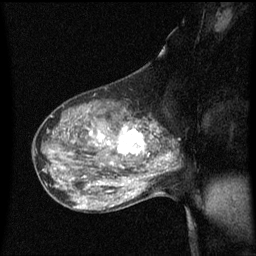
Breast MRI (dynamic contrast-enhanced), one sagittal slice. Position 37 of 60 along the scan axis. Dynamic contrast-enhanced series, image 2 of 3 at this slice position (ordered by acquisition). 1.5 T. TE 4.2 ms, TR 8.4 ms. 2 mm slice thickness. 256 × 256 image matrix, field of view 200 × 200 mm. Female patient, age 50 years.
Structures marked on this image (semi-automatic segmentation, software-assisted and operator-edited):
- analysis volume of interest (the breast-tissue region the enhancement analysis was run in; not a lesion): bounding box <100,114,153,171> (left, top, right, bottom; pixels)
- tumour enhancement mask (voxels above the 70 % enhancement threshold inside the analysis volume of interest): <100,122,153,171>